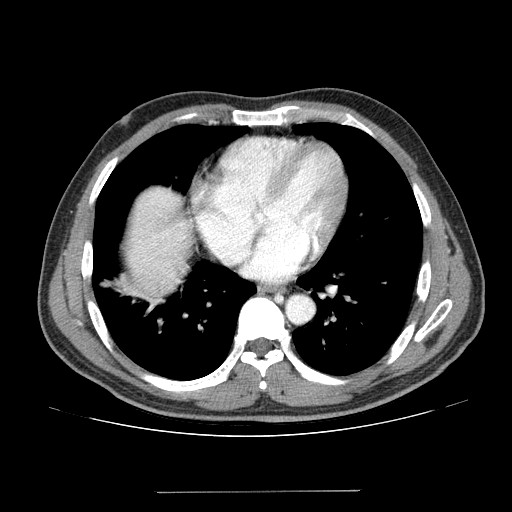
Contrast-enhanced abdominal CT (liver protocol), one axial slice. Position 124 of 131 along the scan axis. Reconstruction kernel STANDARD. One of 2 acquisitions stored at this slice position. Soft-tissue window (W 400 / L 40 HU). 2.5 mm slice thickness. 512 × 512 image matrix, field of view 380 × 380 mm. Case-level facts recorded for this patient, not image findings: diagnosis: hepatocellular carcinoma (patient treated with transarterial chemoembolisation; whether this scan precedes or follows treatment is not stated here); TNM stage (as recorded): Stage-I; Child-Pugh class: A; tumour nodularity: uninodular; tumour size: 10.3 cm.
Structures marked on this image (semi-automatically segmented with operator editing):
- liver parenchyma outside the tumour (the mass and vessels are separate outlines, so this box may not span the whole liver): bounding box (x1, y1, x2, y2) in pixels: (126, 188, 190, 296)
- liver vessels: (183, 237, 185, 239)